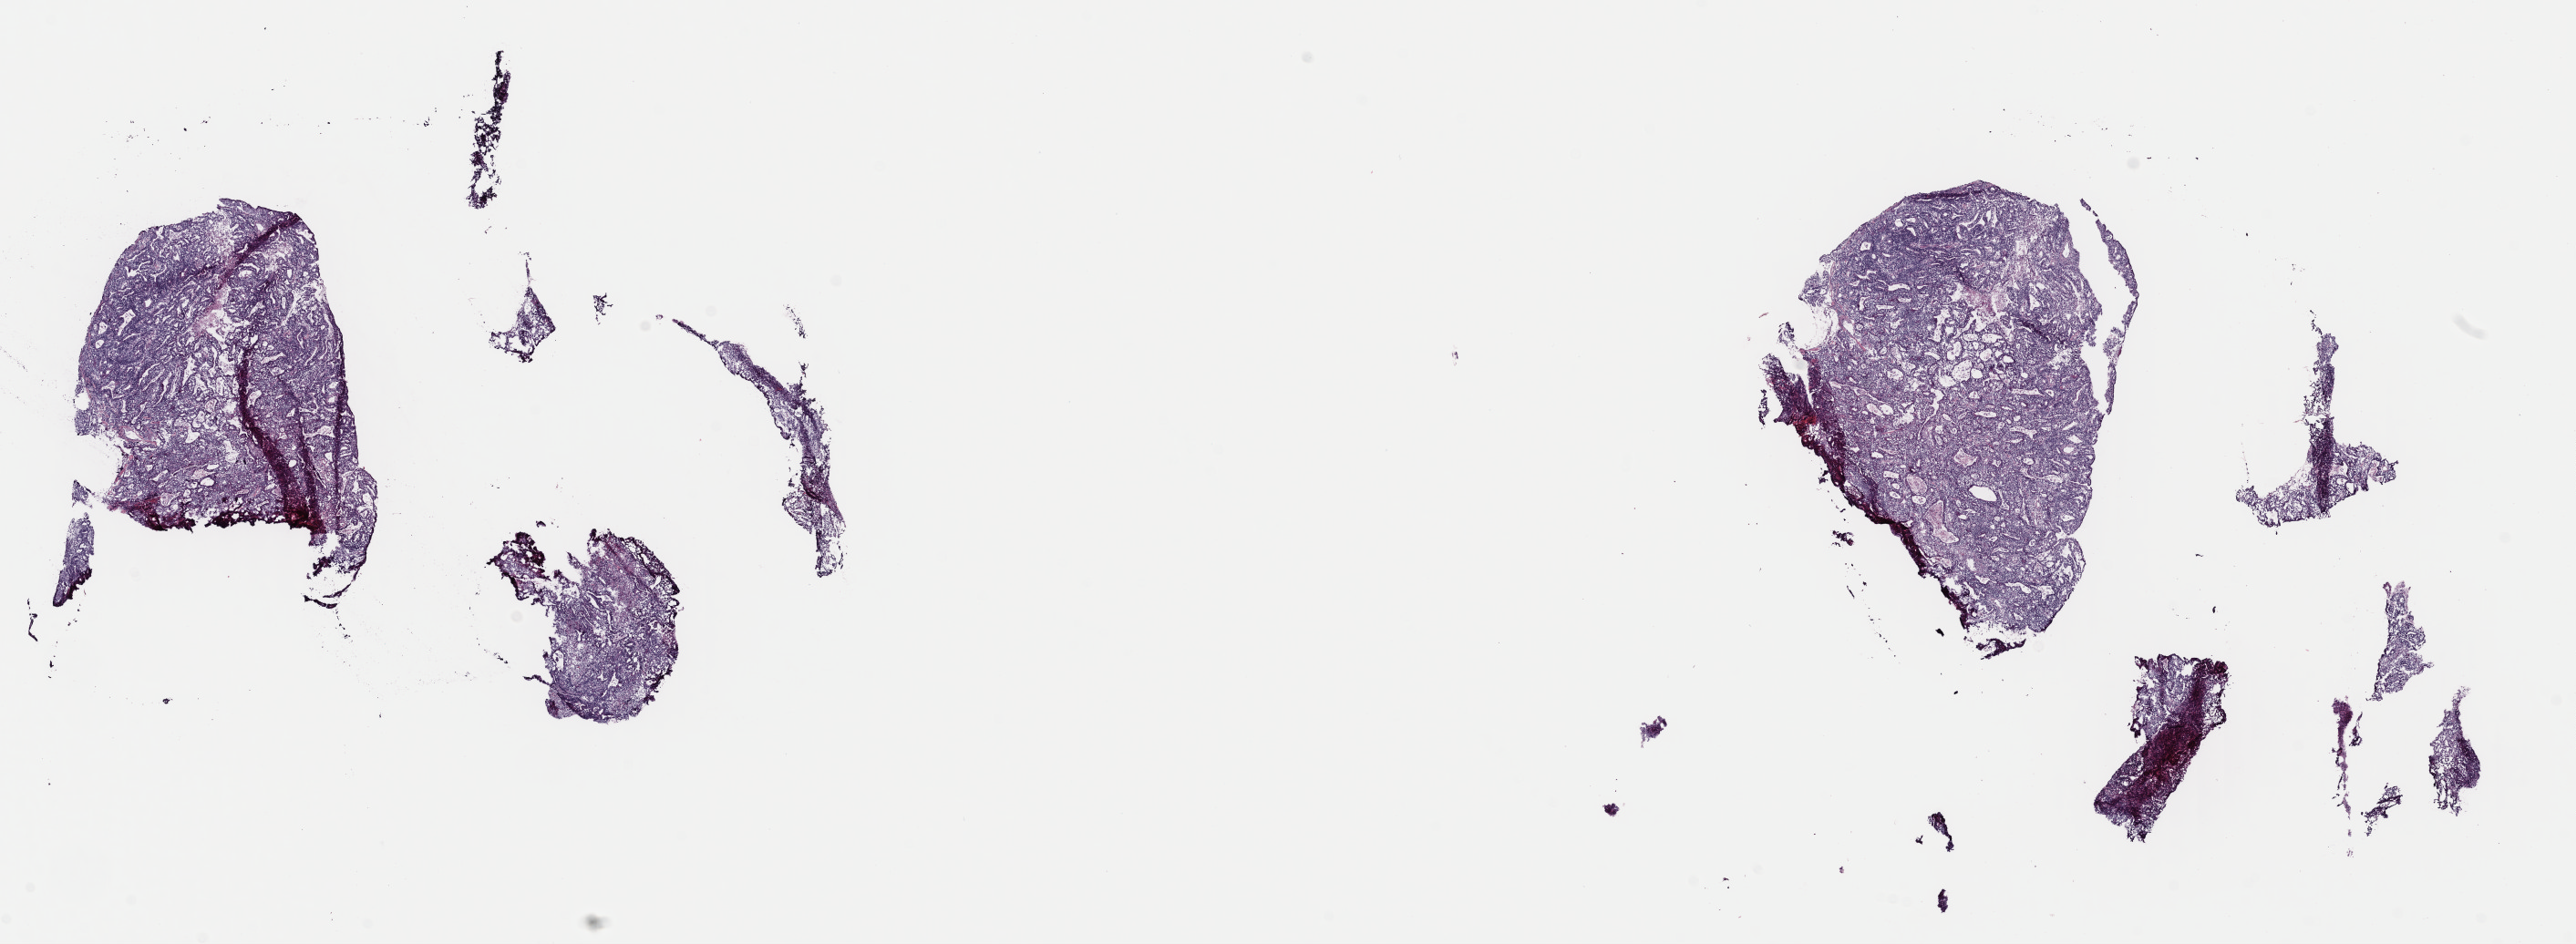
Digitized Hematoxylin and eosin (H&E) stained tissue section (whole slide) — a low-resolution overview of the entire scanned area, about 22.3 x 8.2 mm (from a 40x scan), frozen section from the top of the tissue portion, sample: primary tumour, cervix. Patient: female, age at initial diagnosis 44 years. Histologic grade: GX (grade cannot be assessed). Pathologist review of this section (percent, as recorded): tumour cells 100%, tumour nuclei 80%, normal cells 0%, stromal cells 0%, necrosis 0%. Inflammatory infiltration, as recorded: lymphocyte infiltration 2%, monocyte infiltration 0%, neutrophil infiltration 0%.
FIGO stage: IB2. Histologic diagnosis: Adenocarcinoma, endocervical type.